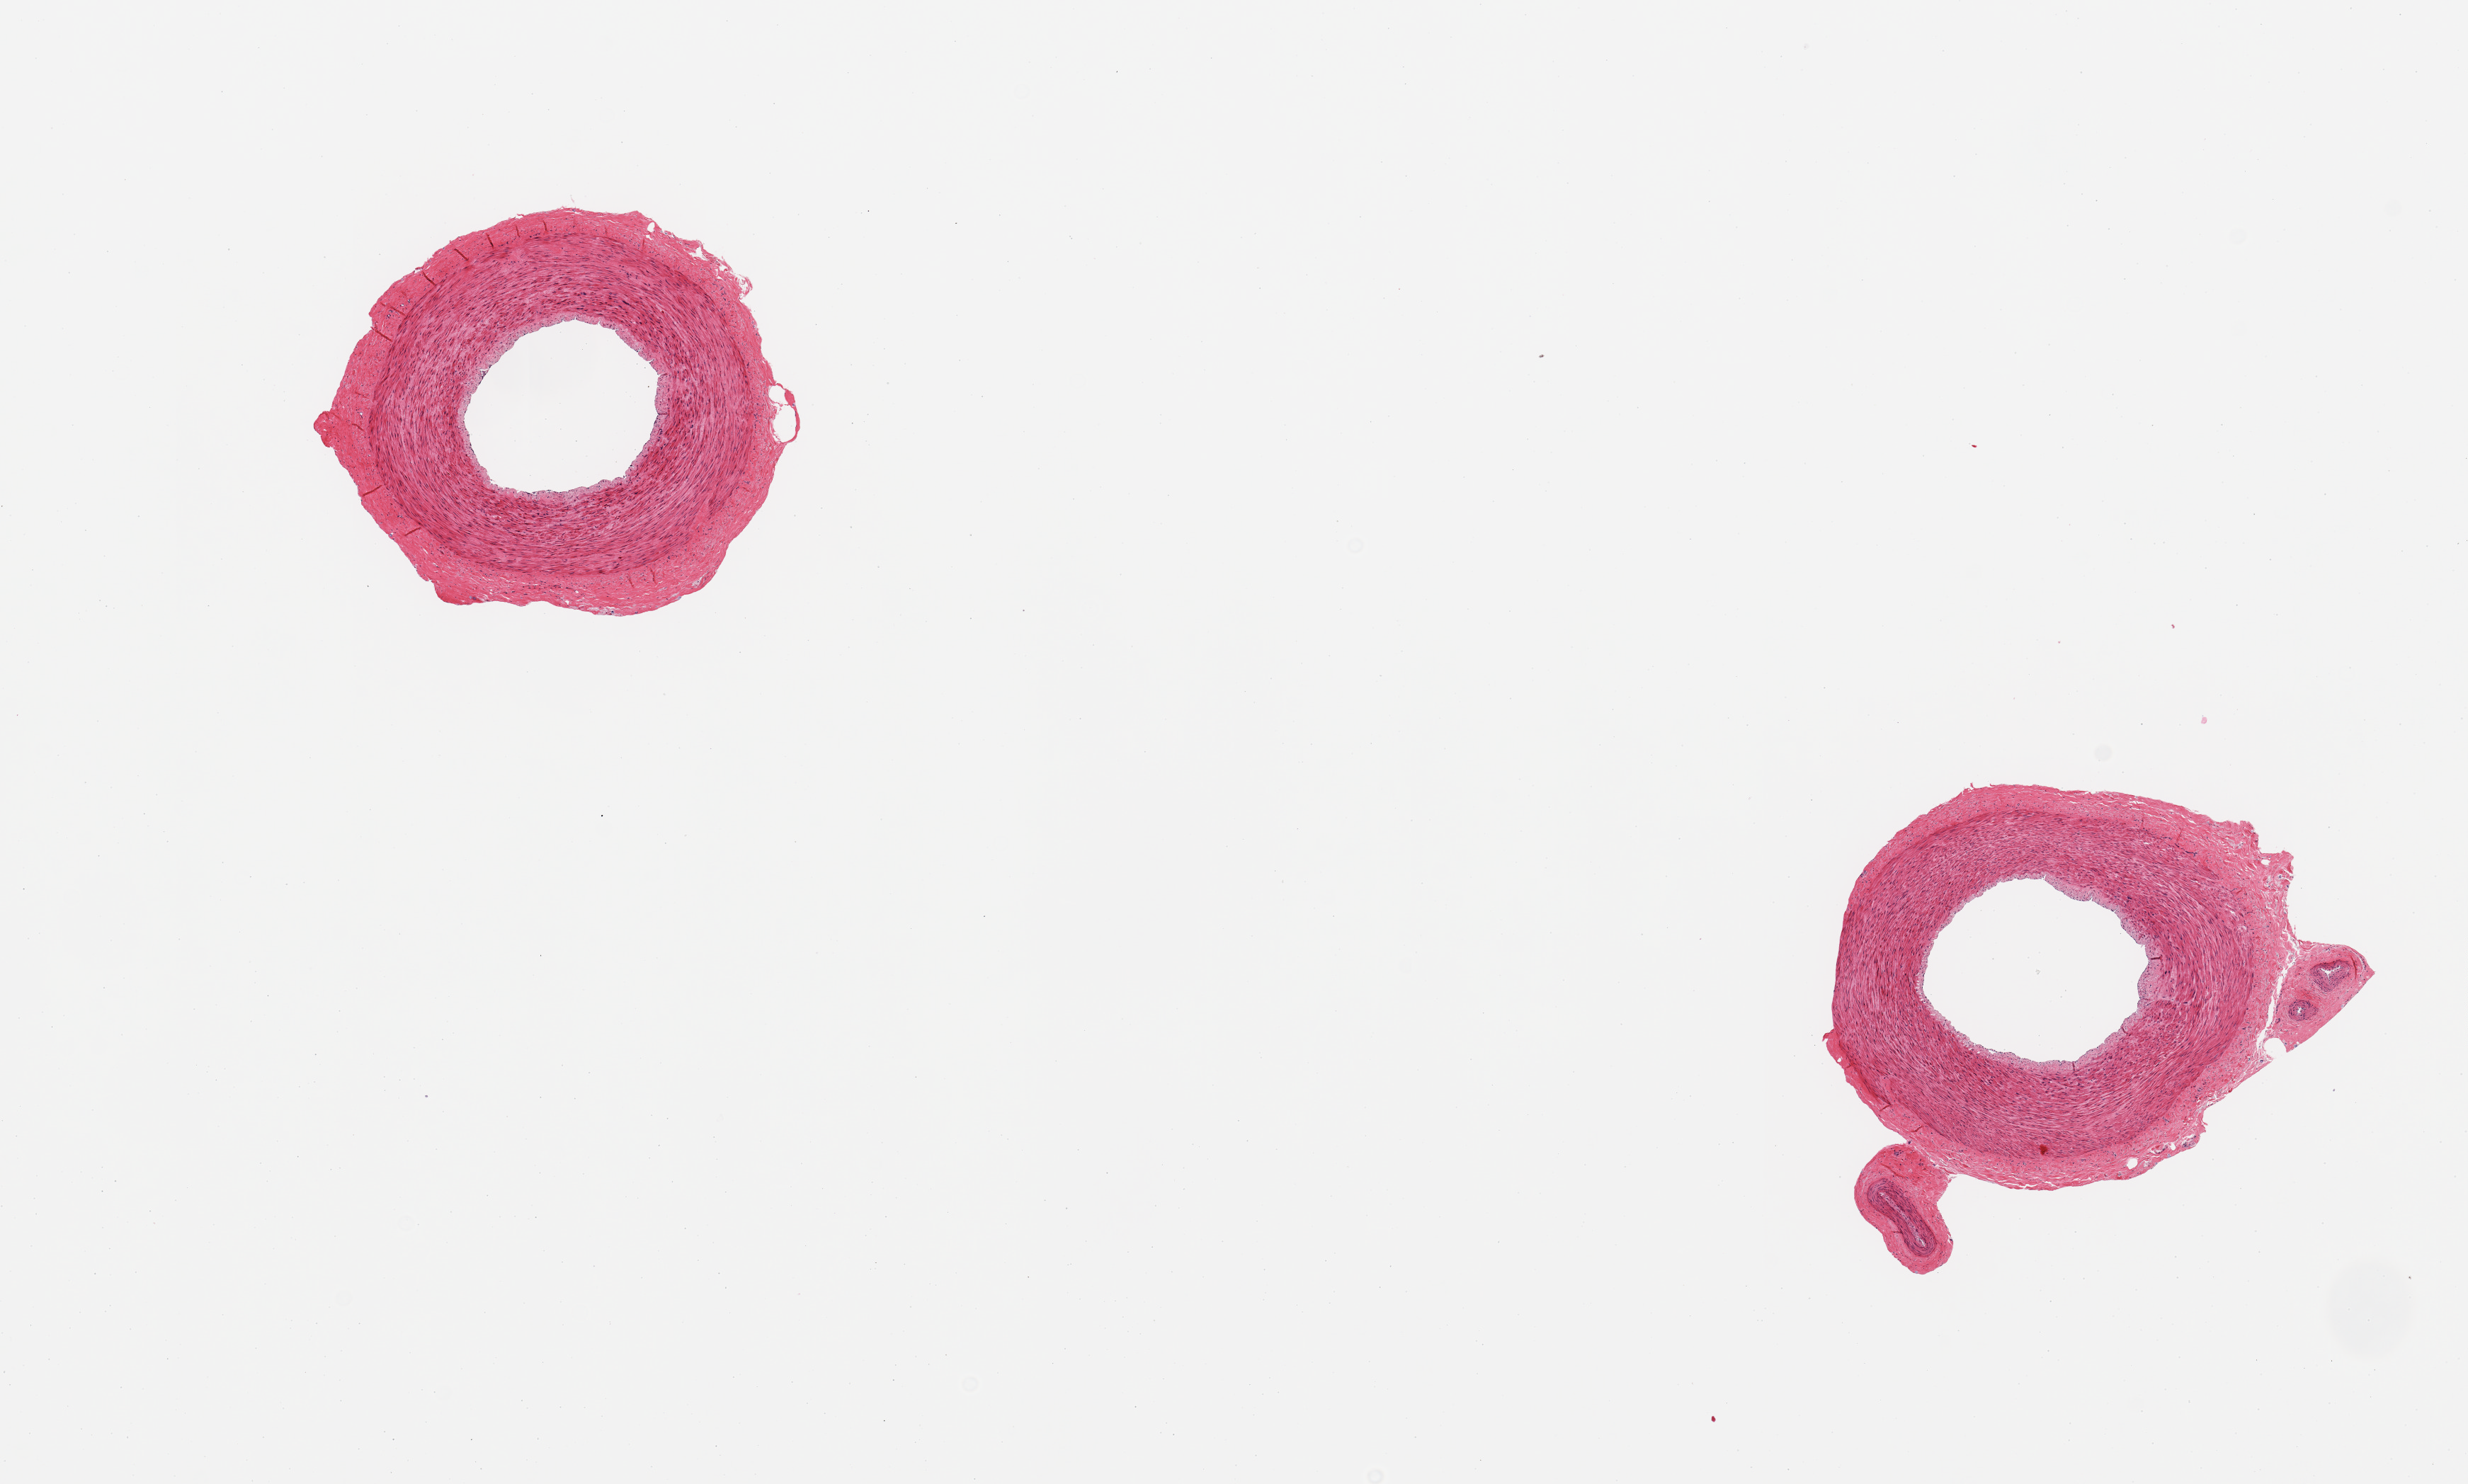
Digitized hematoxylin and eosin (H&E)-stained section, low-resolution overview of the scanned area, about 13.8 x 8.3 mm. PAXgene-fixed paraffin-embedded (PFPE) section. Sampled site (target tissue): tibial artery. Tissue donor sample. Donor: male.
• reviewer comment on this tissue sample: 2 pieces, no atherosis, no adherent fat, excellent specimen